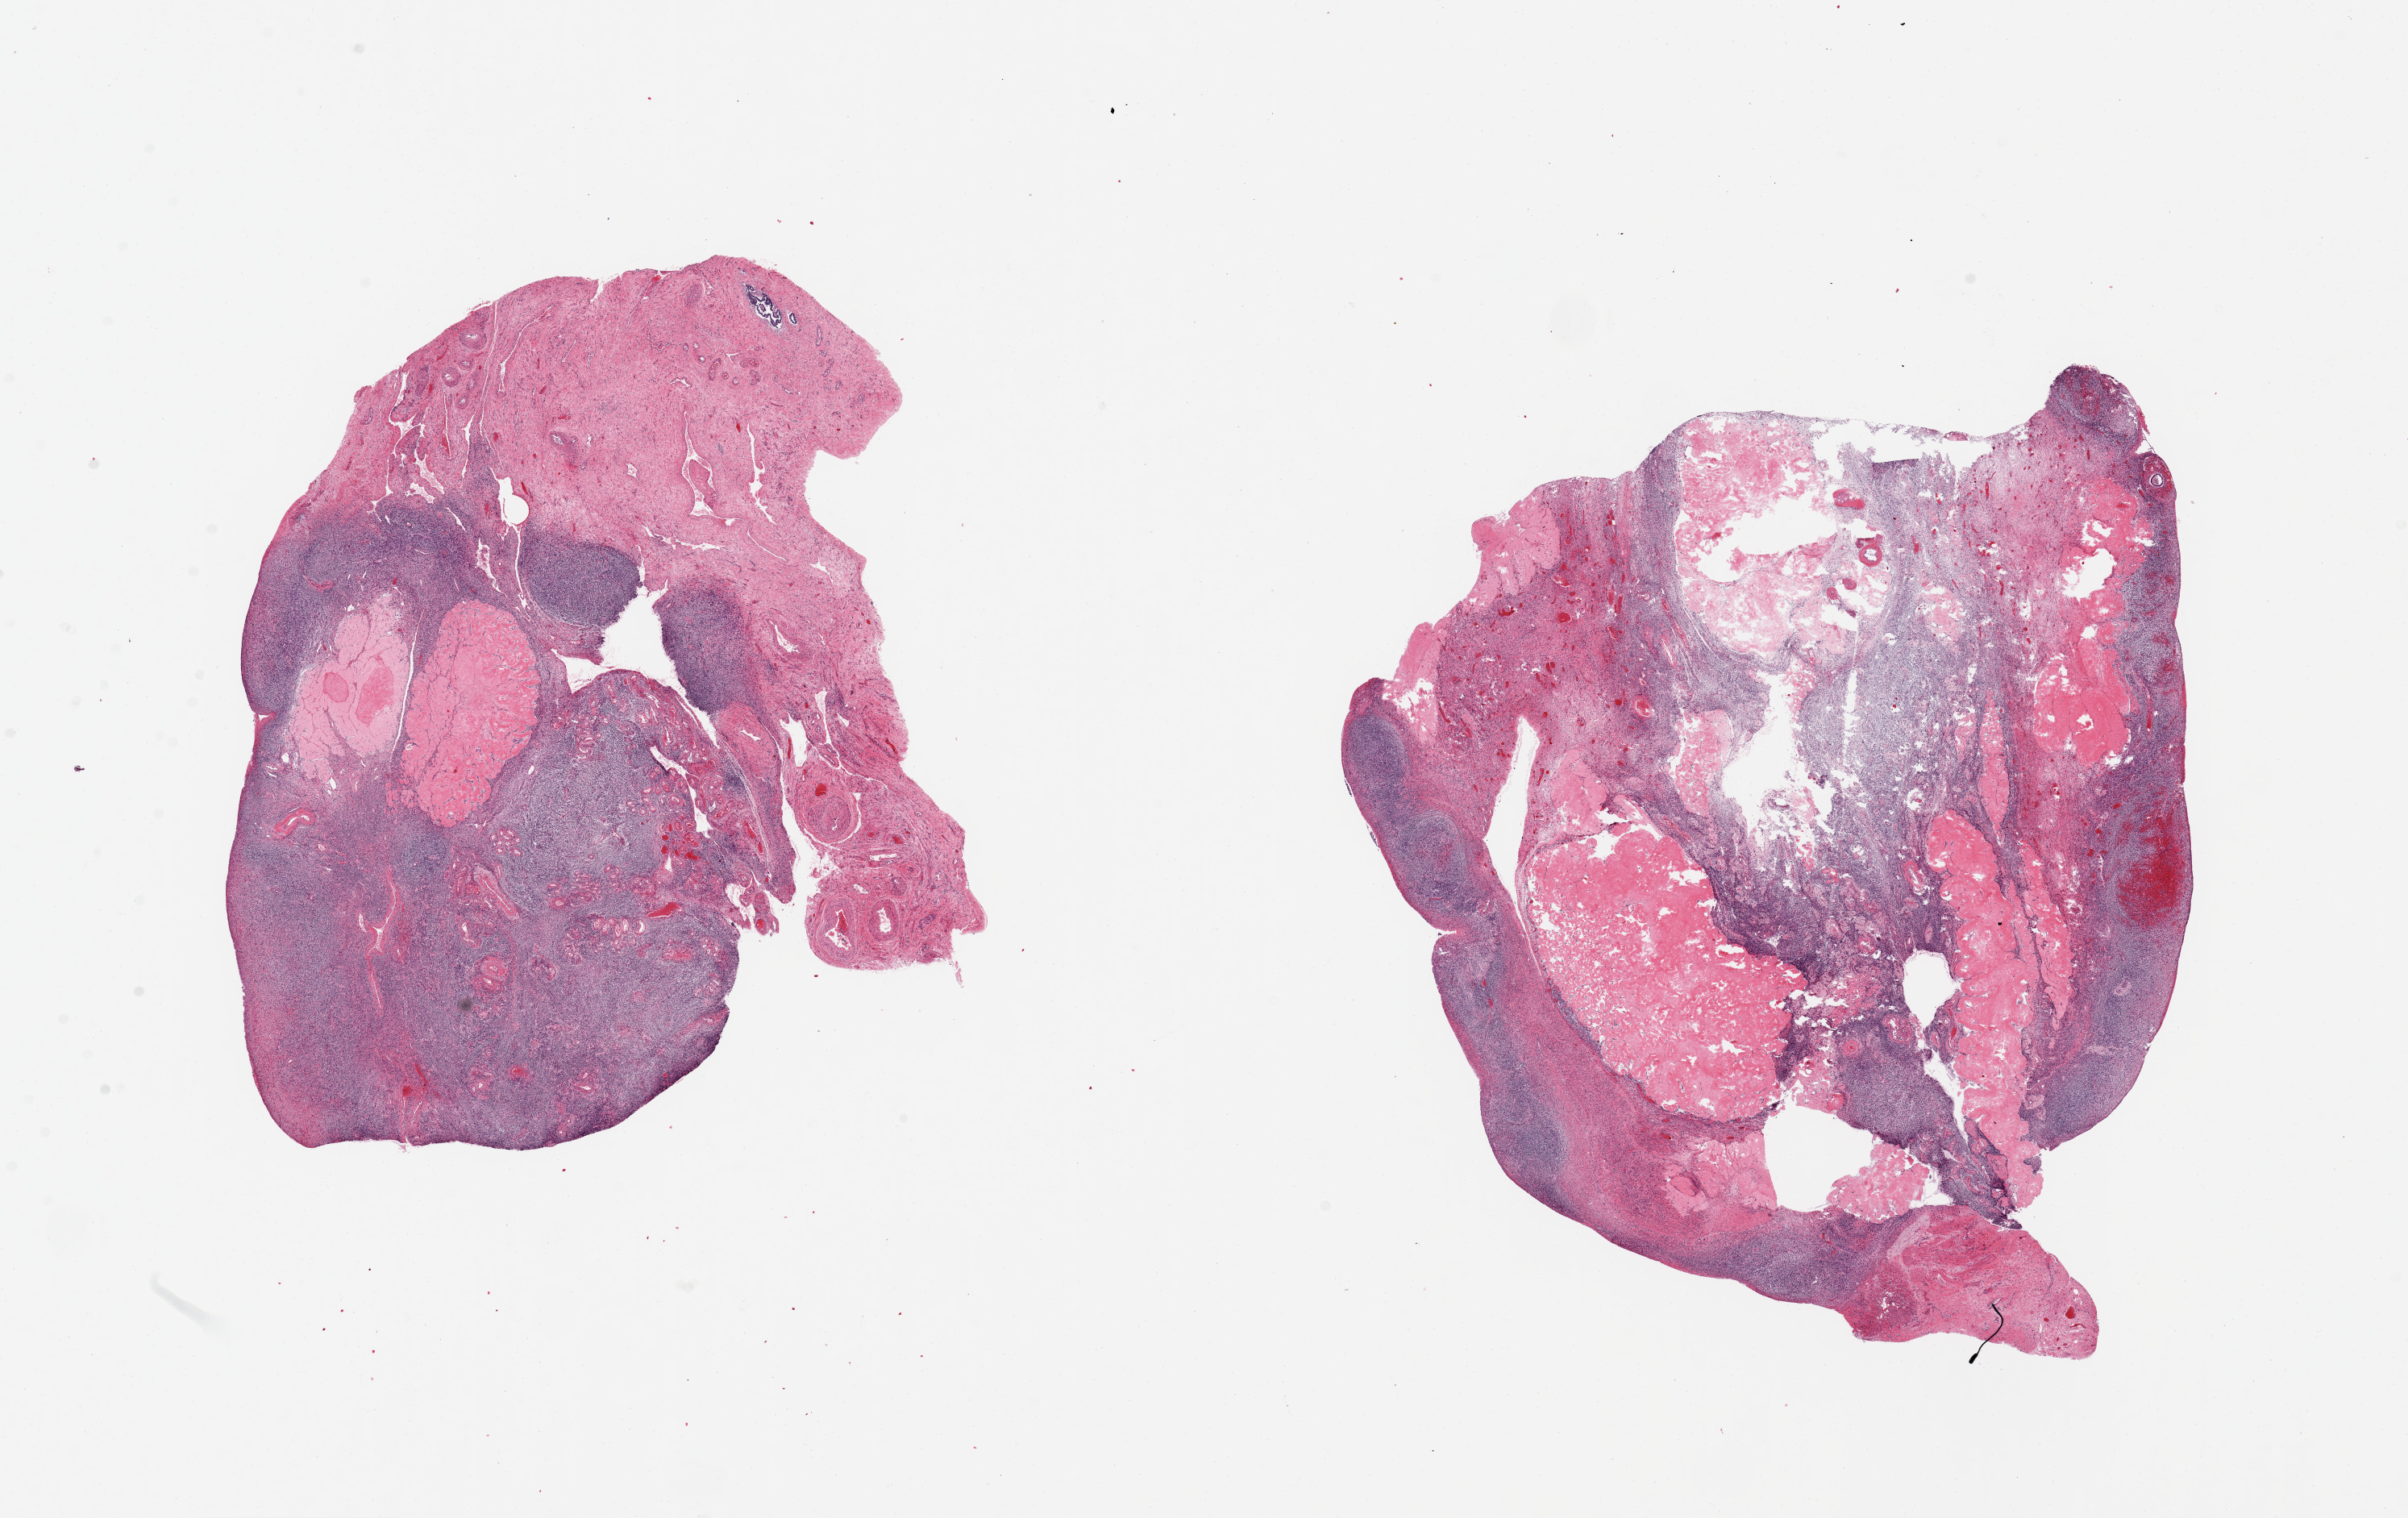
Digitized haematoxylin and eosin-stained section — low-resolution overview of the scanned area, about 23.6 x 14.9 mm (from a 20x scan); PAXgene-fixed paraffin-embedded (PFPE) section; sampled site (target tissue): ovary; tissue donor sample.
• review note (as recorded): 2 pieces, 9.5x7 & 10x8mm; Atrophic; corpora albicans